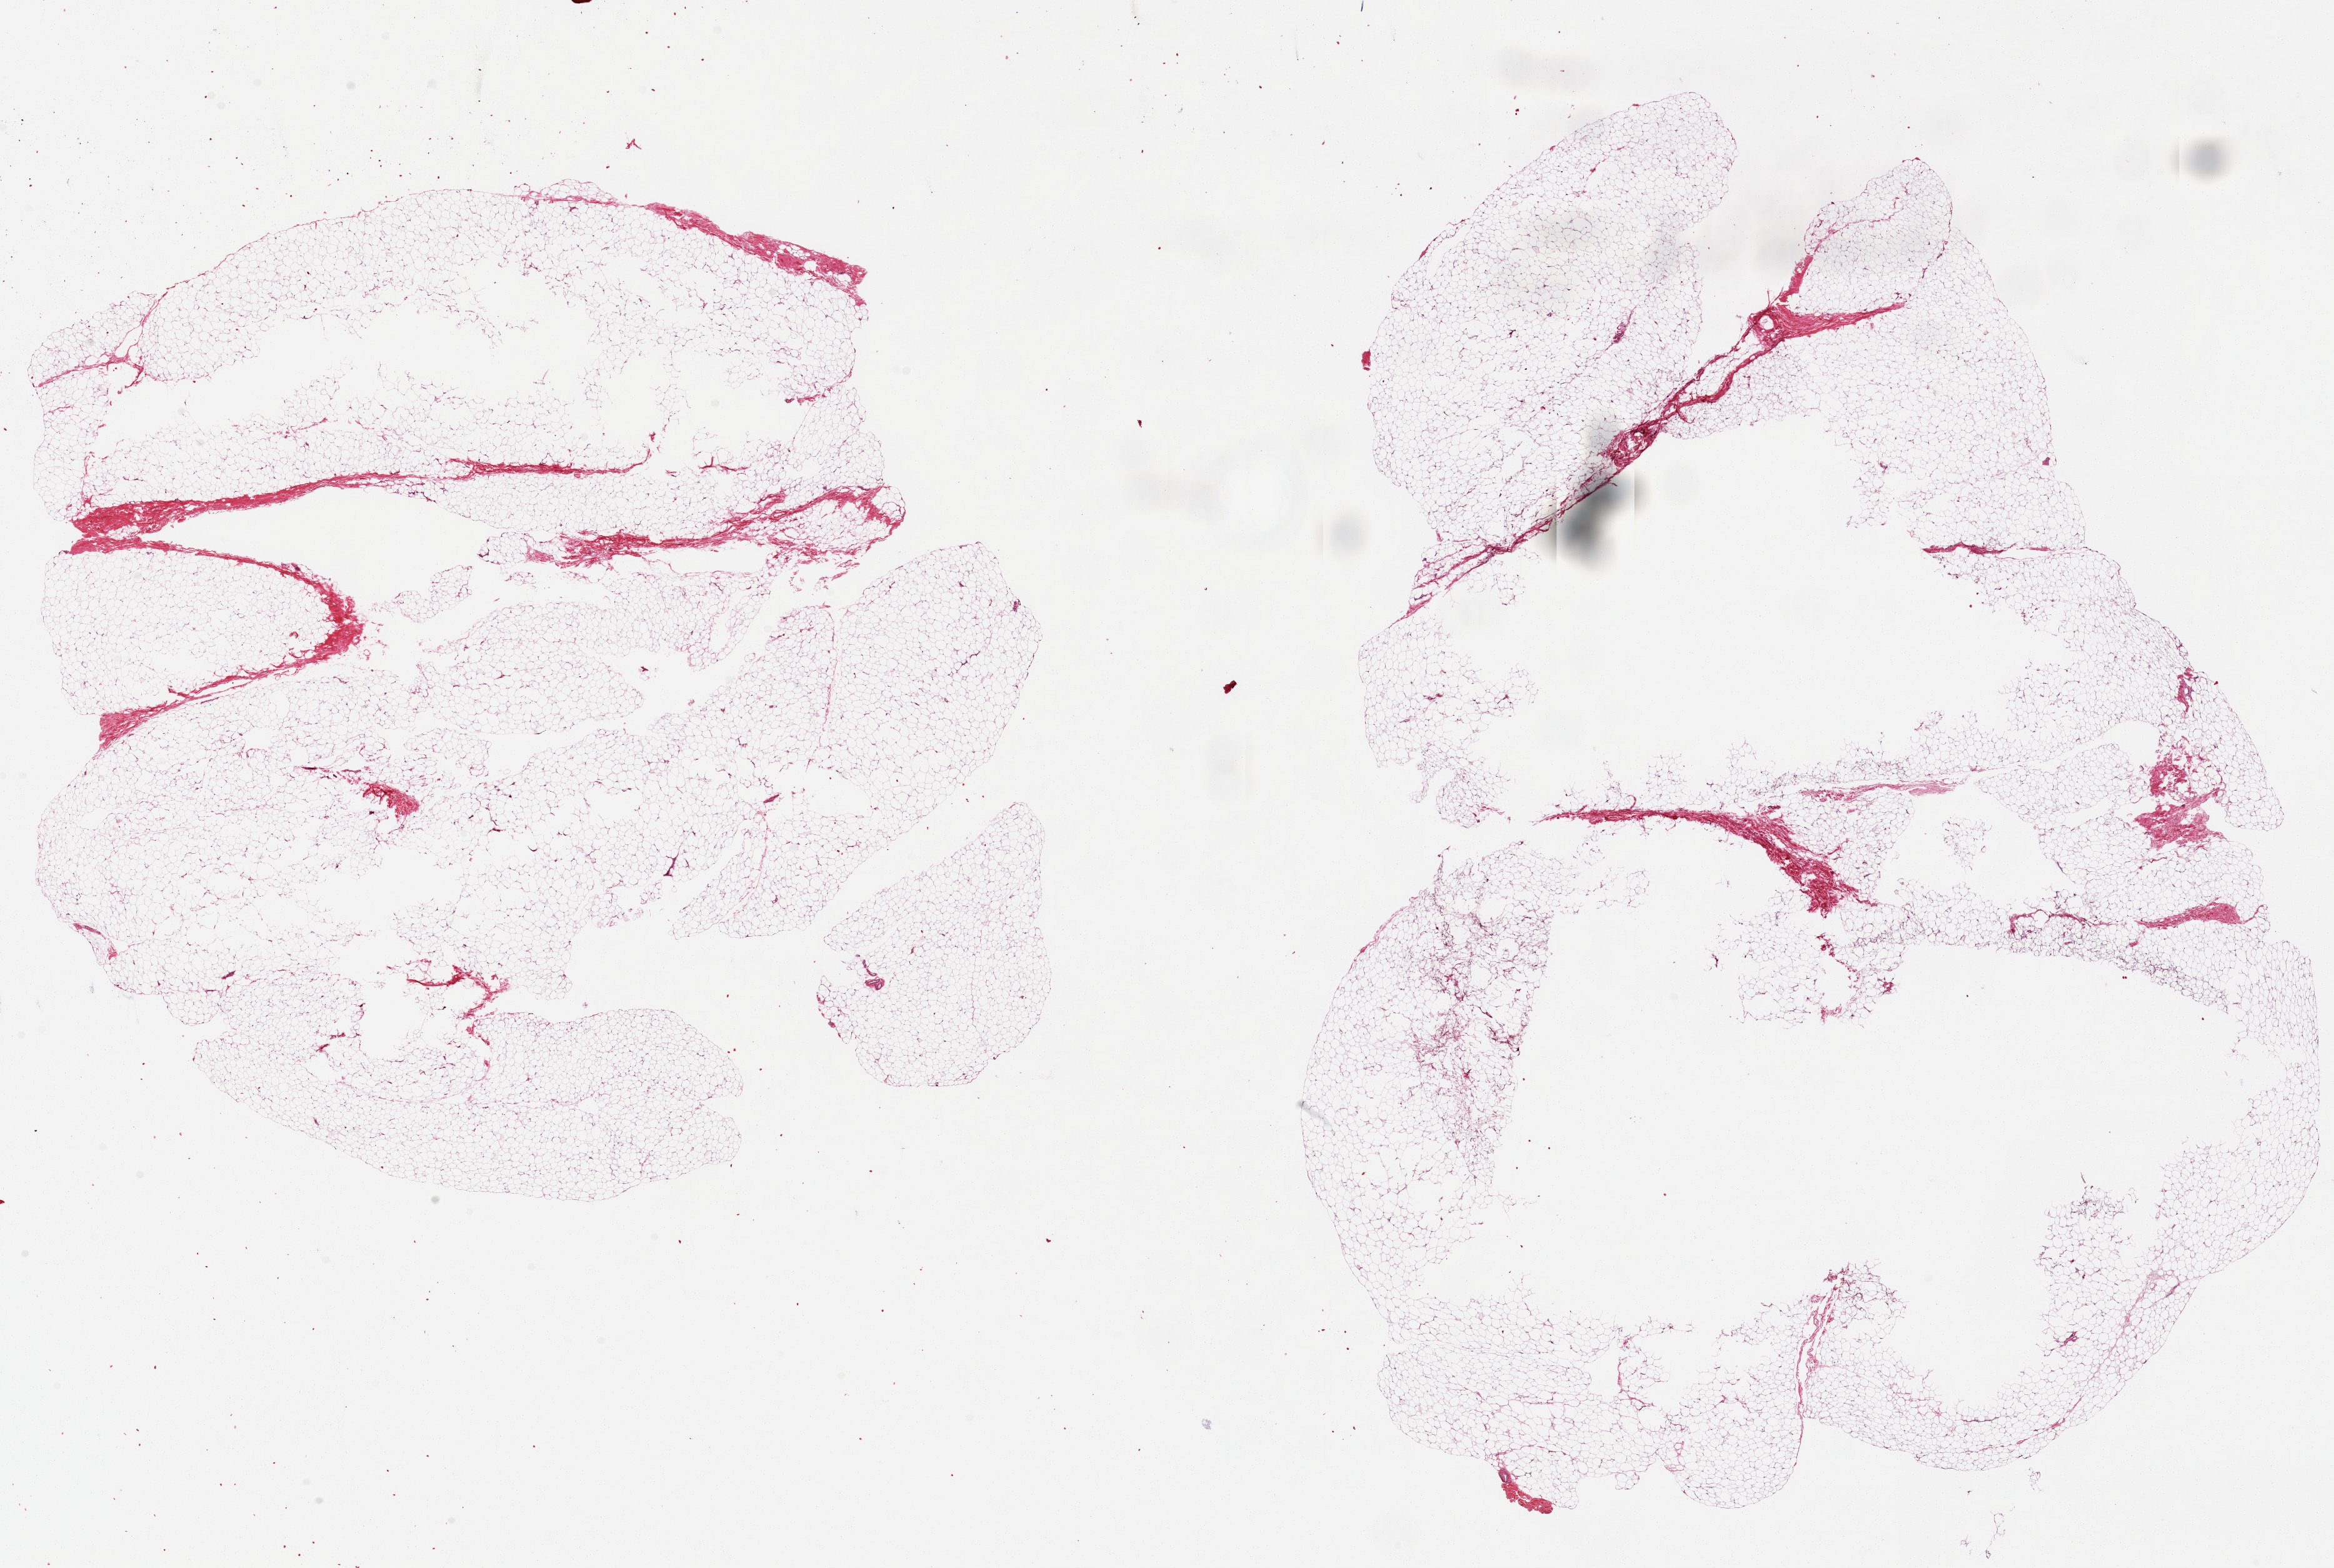
Digitized hematoxylin and eosin (H&E)-stained section, whole scanned area (about 29.5 x 19.8 mm) shown as a low-resolution overview; PAXgene-fixed, paraffin-embedded tissue; target tissue: adipose tissue; donor tissue sample.
Review note (as recorded): 2 ~14x12mm aliquots, central separation/under fixation.